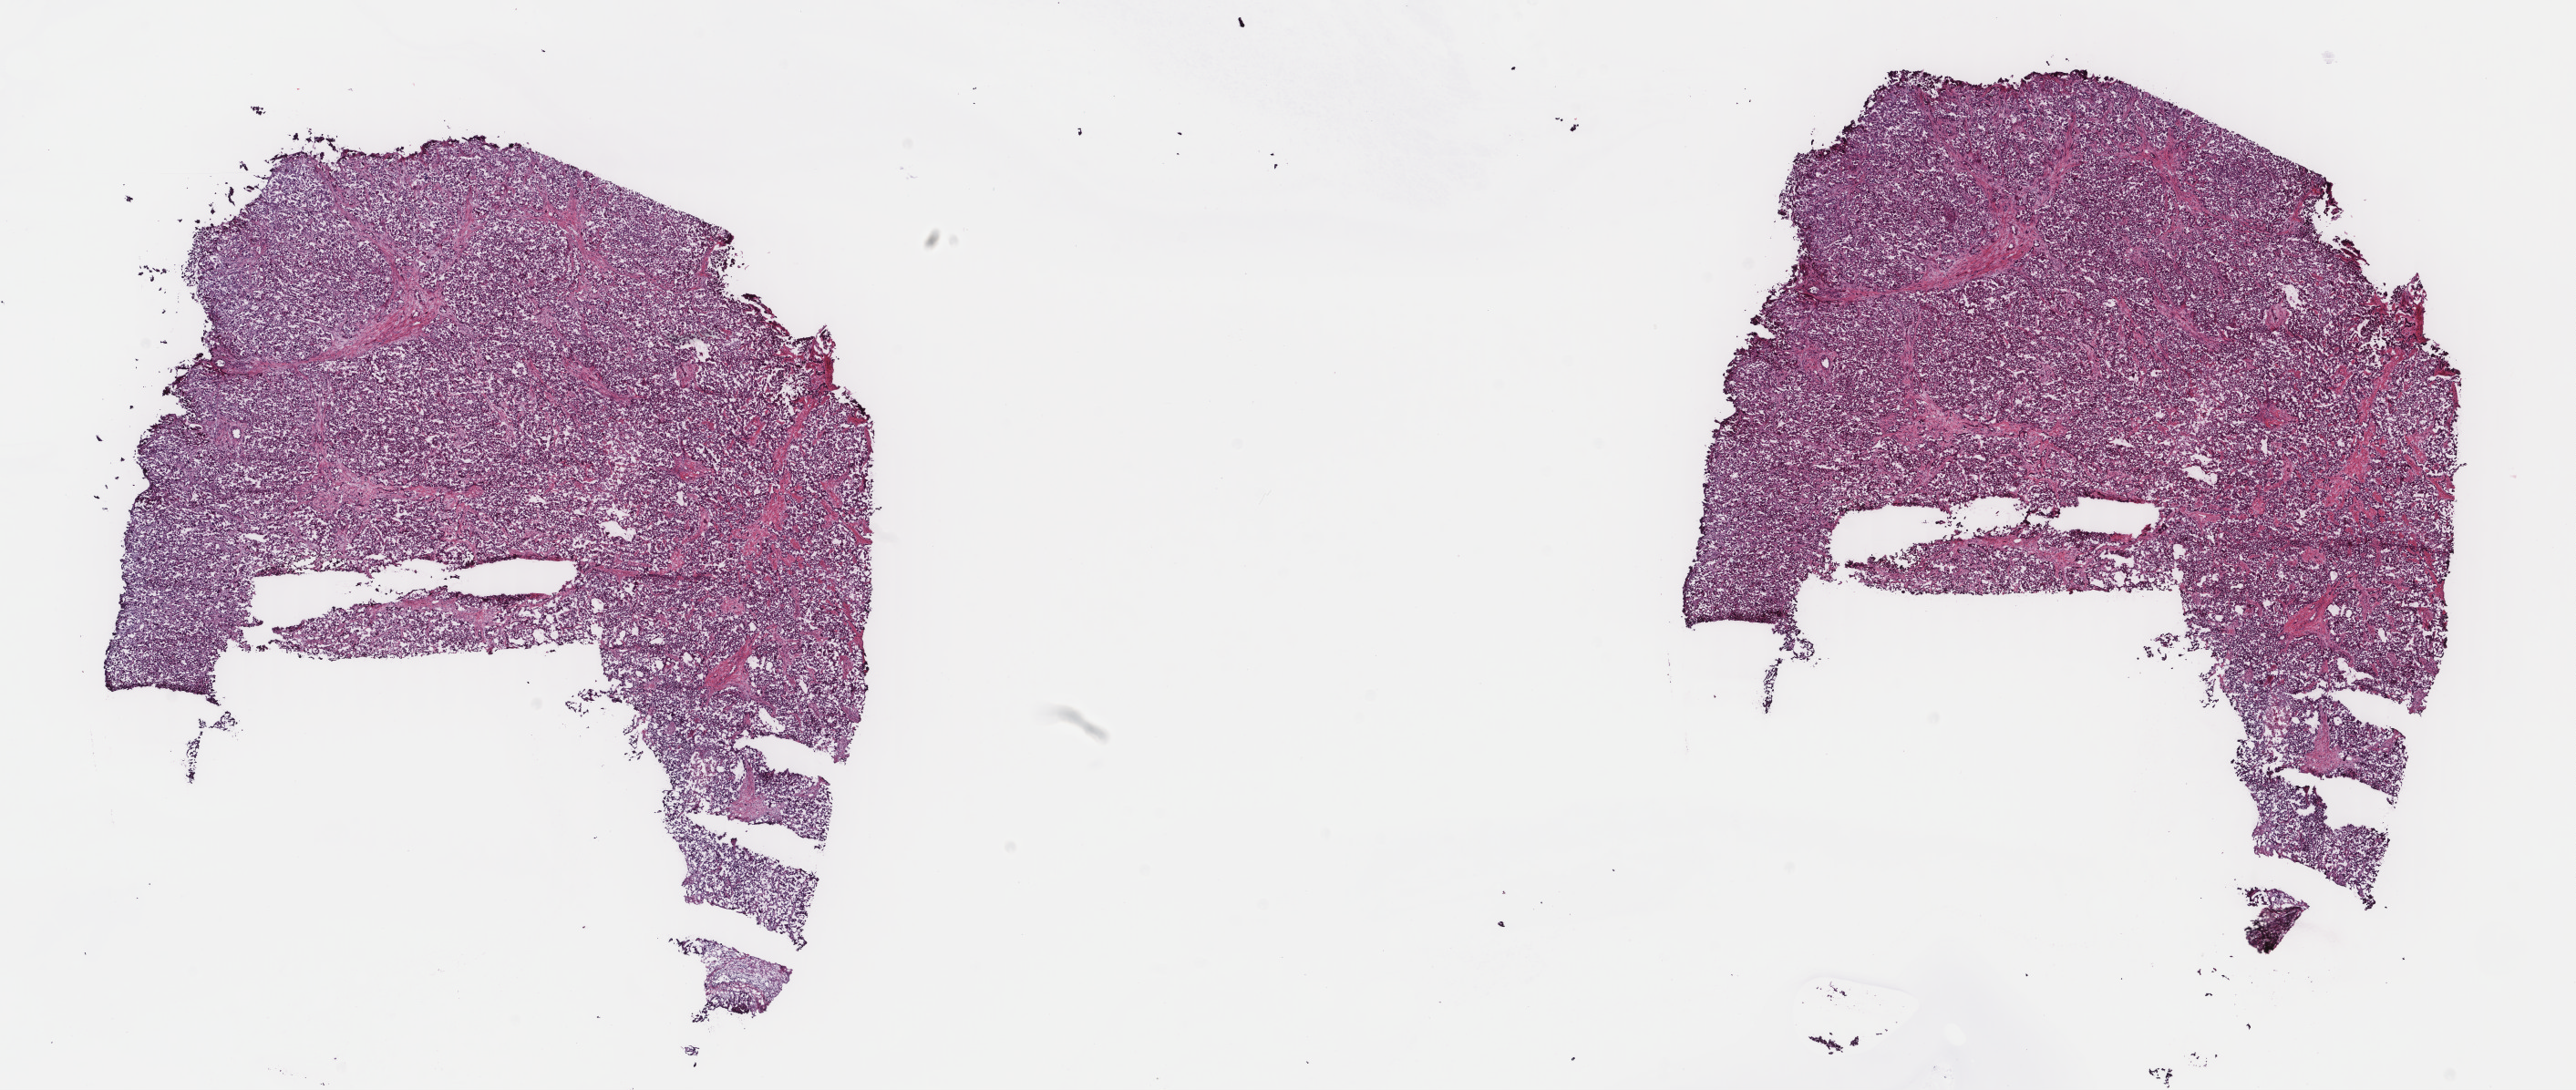
H&E-stained whole-slide image, whole scanned area (about 22.4 x 9.5 mm) shown as a low-resolution overview. Frozen section from the top of the tissue portion. Liver, primary tumour sample. Patient: female, age at initial diagnosis 45 years. Histologic grade: G2 (moderately differentiated). Pathologist review of this section (percent, as recorded): tumour cells 100%, tumour nuclei 95%, normal cells 0%, stromal cells 0%, necrosis 0%. Infiltration values recorded for this section: lymphocyte infiltration 0%, monocyte infiltration 0%, neutrophil infiltration 0%.
• AJCC pathologic stage: IIIA
• diagnosis: Hepatocellular carcinoma, NOS